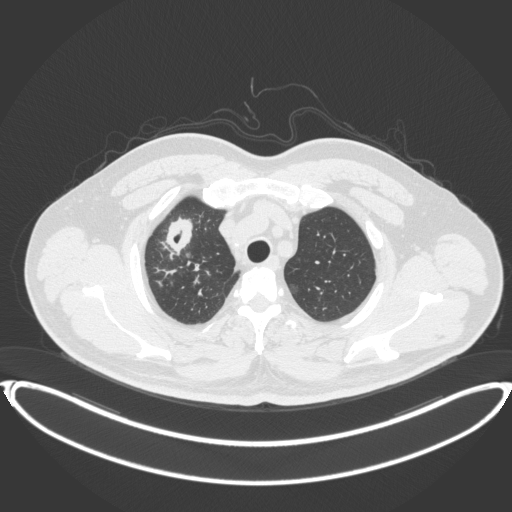
Chest CT, one axial slice. 120 kVp. Lung window (W 1500 / L -600 HU). 1 mm slice thickness. 512 × 512 image matrix. Male patient, age 53 years. Case-level facts recorded for this patient, not image findings: clinical TNM (as recorded): T2a N0 M0.
Structures marked on this image (bounding box drawn by a radiologist):
- lung tumour (recorded histology: adenocarcinoma): bounding box <162,214,198,259> (left, top, right, bottom; pixels)